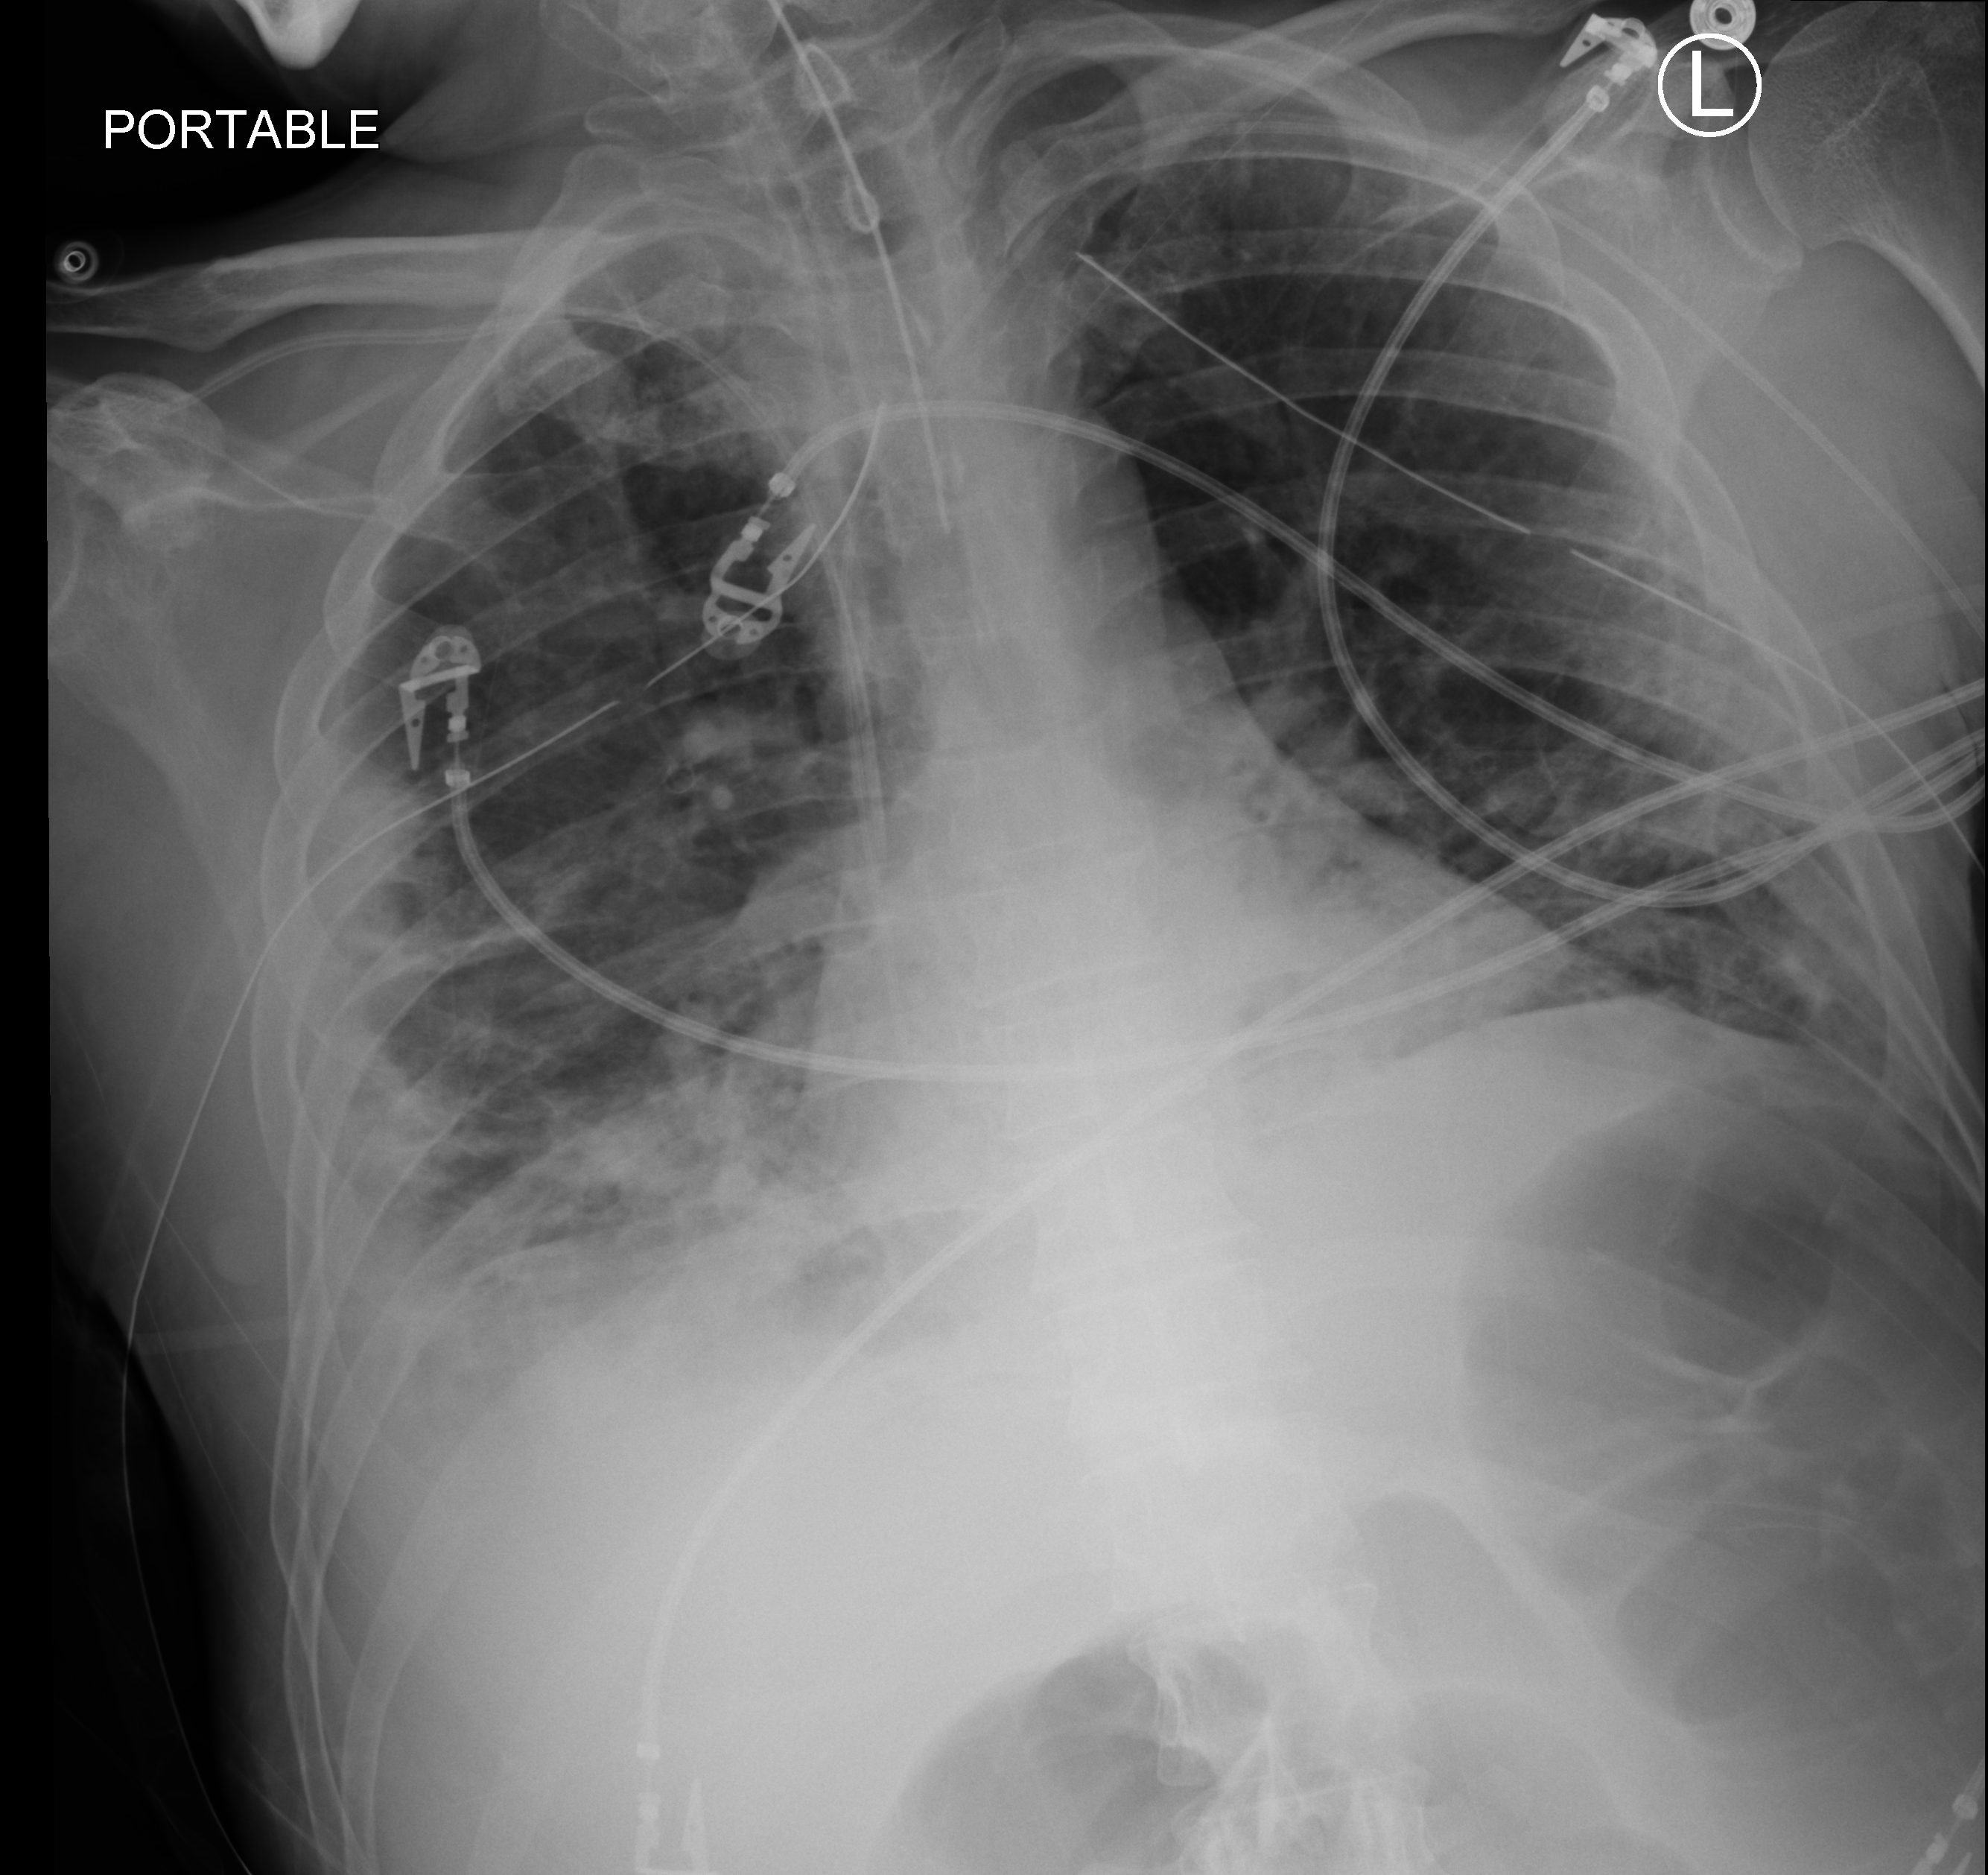
Portable chest radiograph. Patient hospitalised with COVID-19; male, aged 18–59 years.
Admission-level facts for this patient (not findings on this image; timing relative to this image not recorded): admitted to intensive care during this hospital stay: yes; diabetes (admission record): yes; mechanically ventilated during this hospital stay: yes.